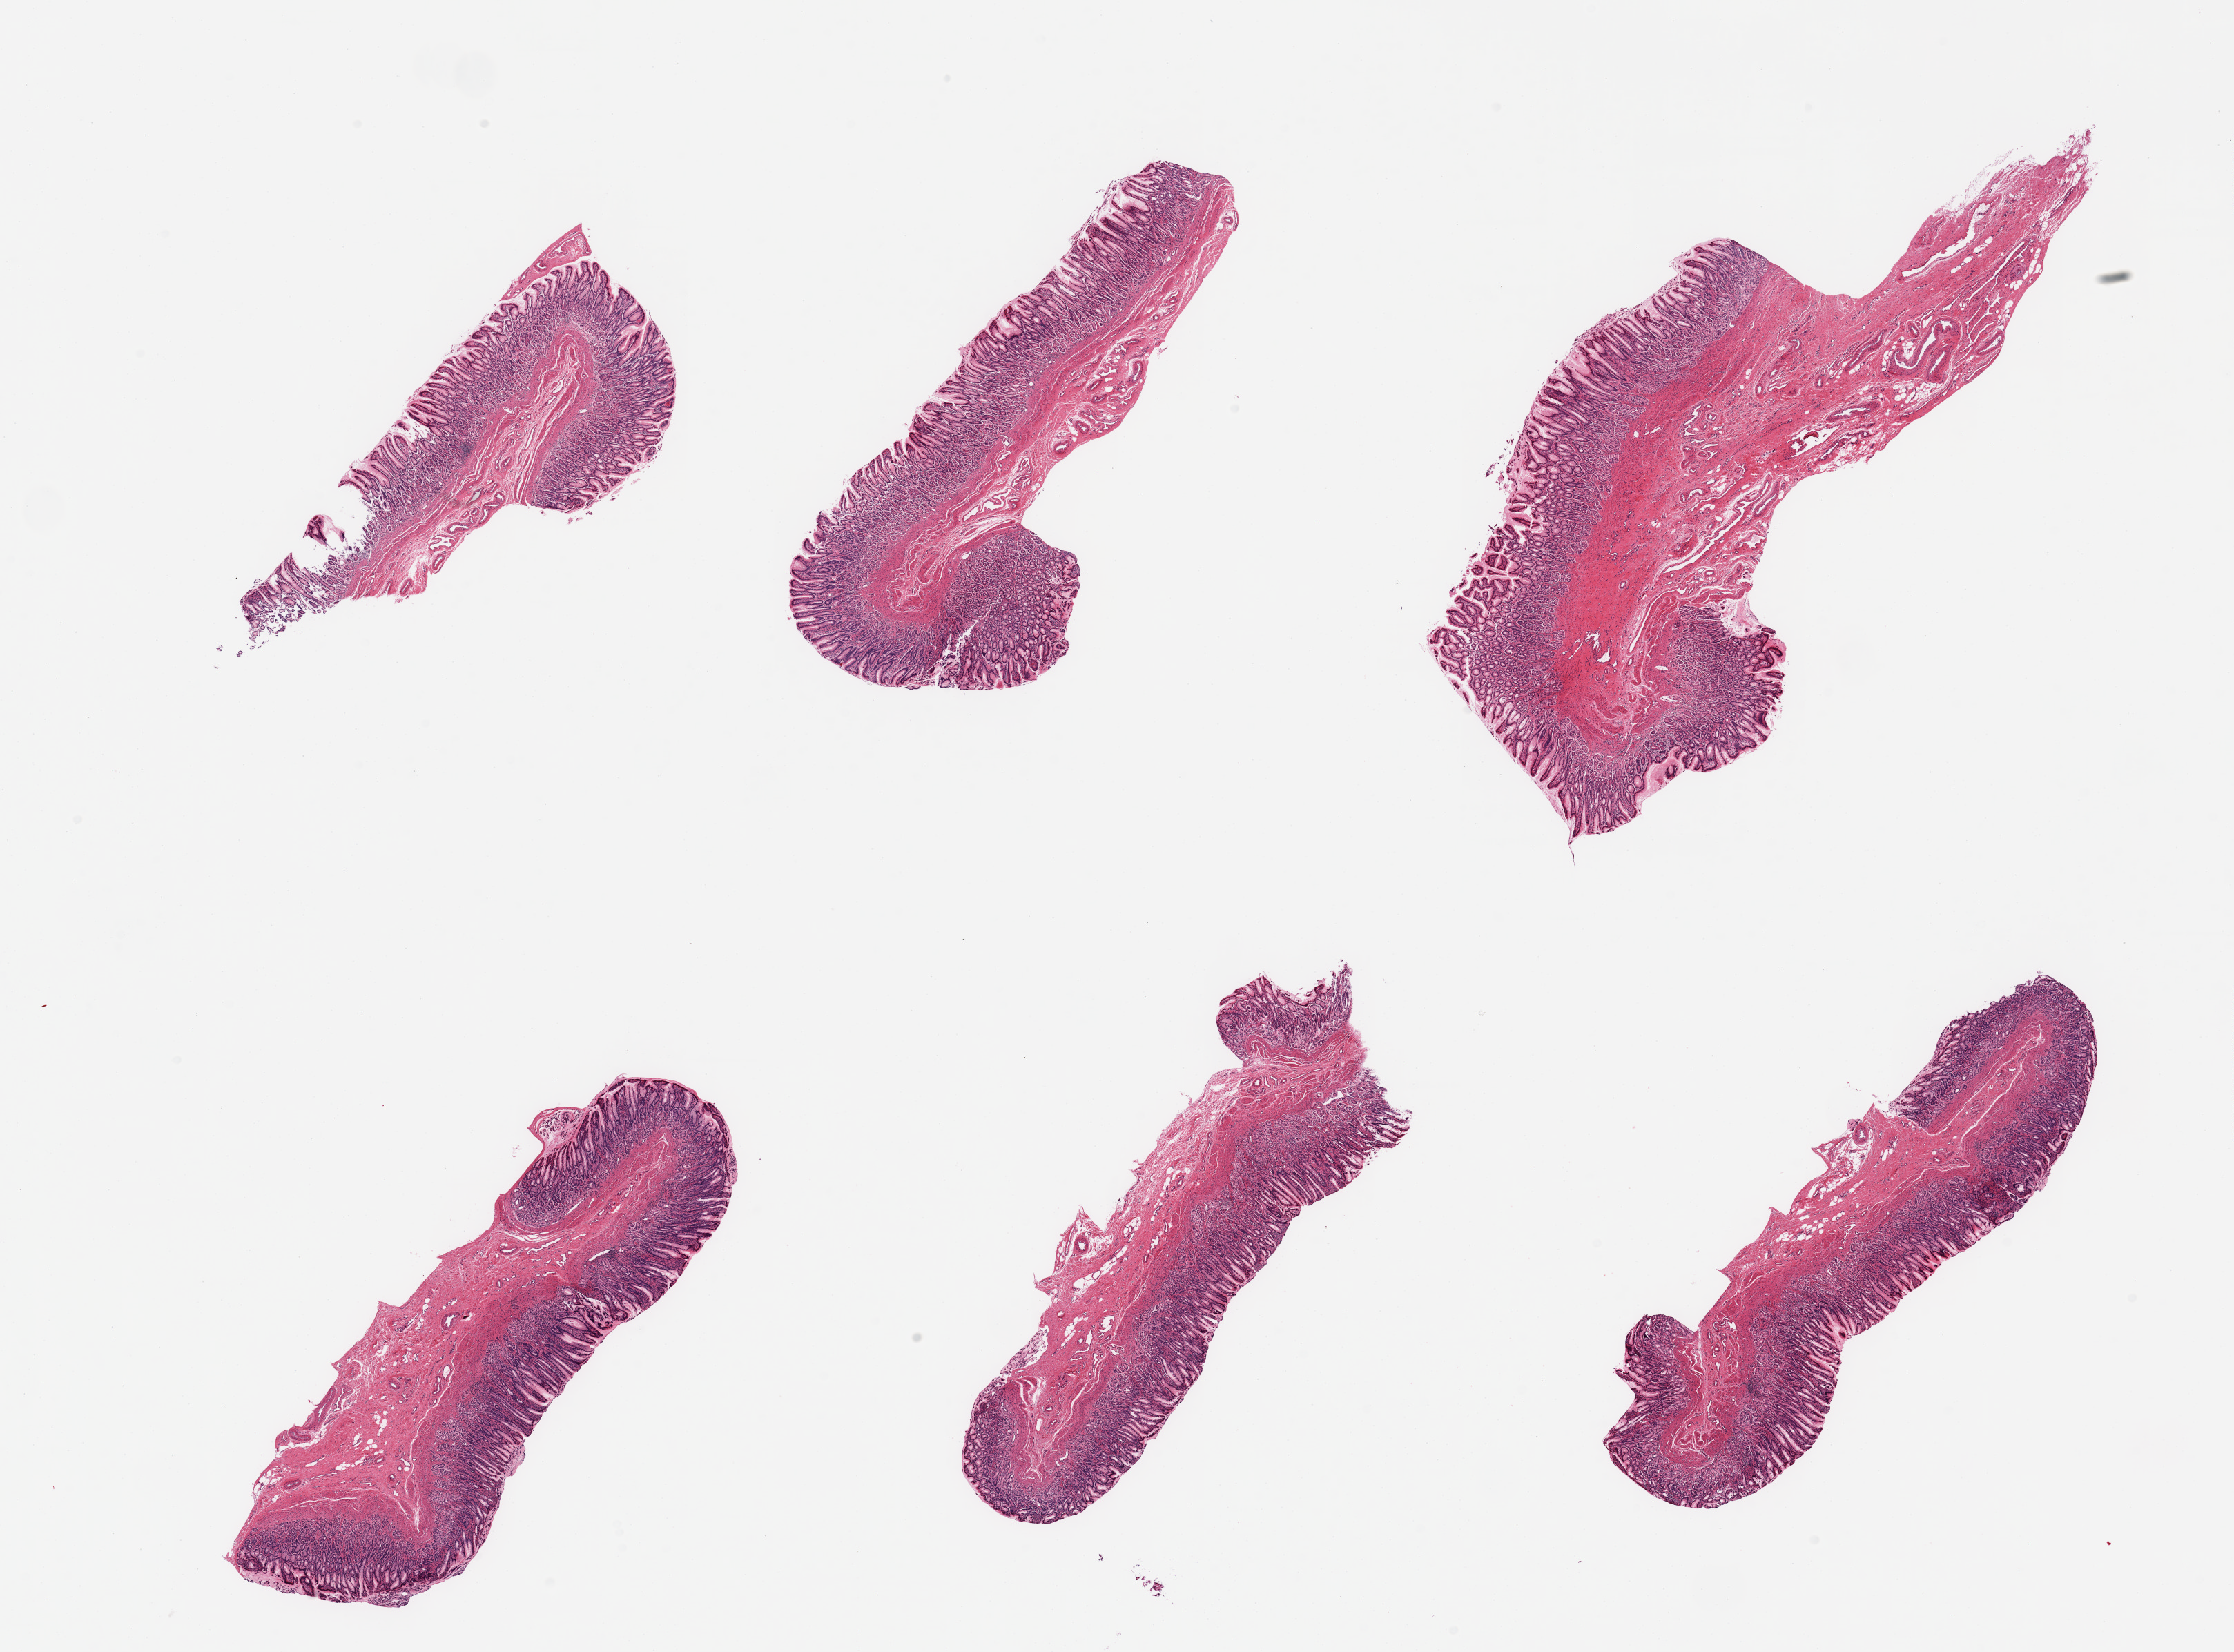
Digitized hematoxylin and eosin (H&E)-stained section — whole scanned area (about 25.6 x 18.9 mm, from a 20x scan) shown as a low-resolution overview, PAXgene-fixed paraffin-embedded (PFPE) section, sampled site (target tissue): transverse colon, donor tissue sample. Donor sex: female.
Reviewer comment on this tissue sample: 6 pieces; mildly autolyzed mucosa and submucosa; muscularis not included.